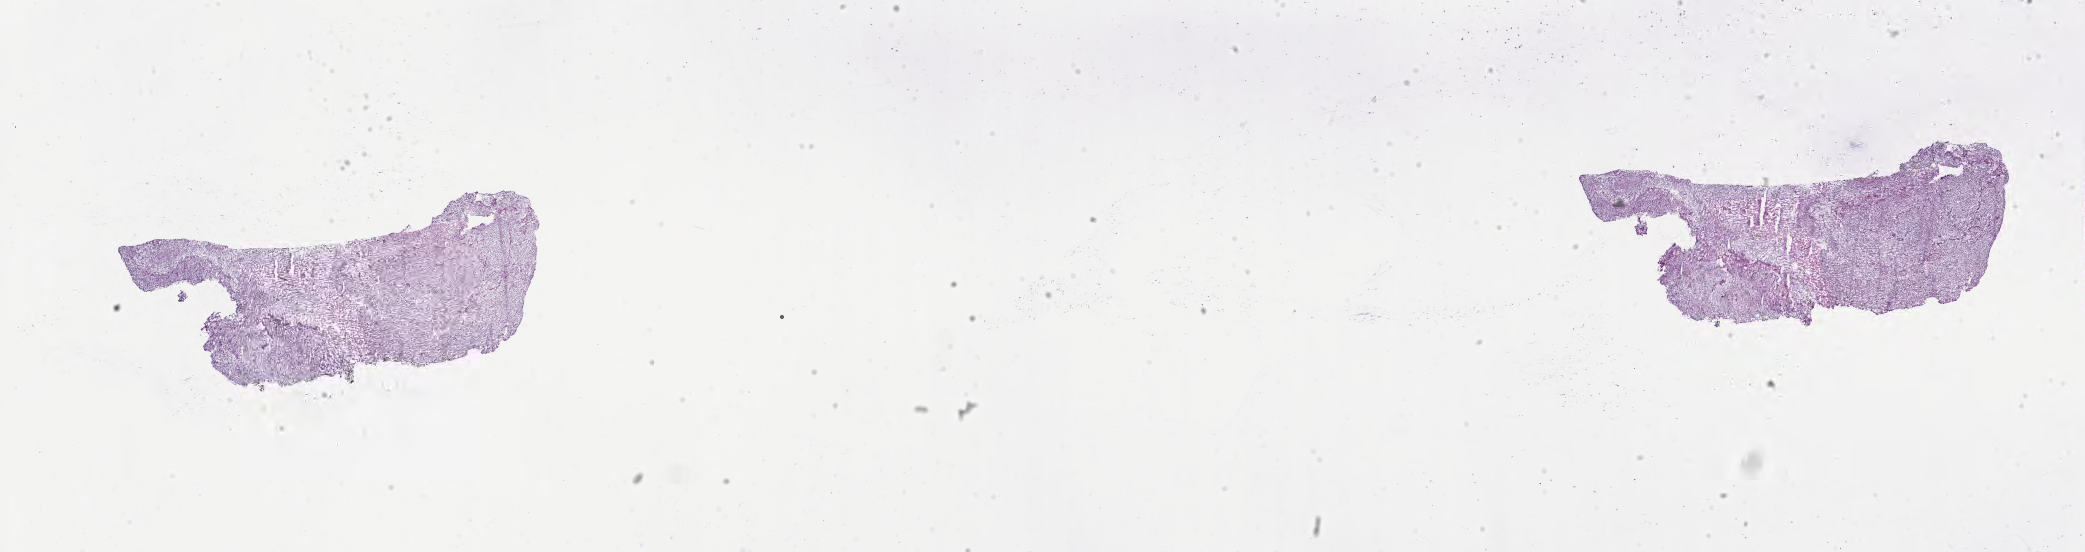
Whole-slide image, haematoxylin and eosin stain of tumor tissue from the brain — shown as a low-resolution overview of the whole scanned area (about 33.7 x 8.9 mm), frozen section. Patient male; age 129 months (10 years 9 months).
* diagnosis (ICD-O-3 morphology term): Glioma, malignant